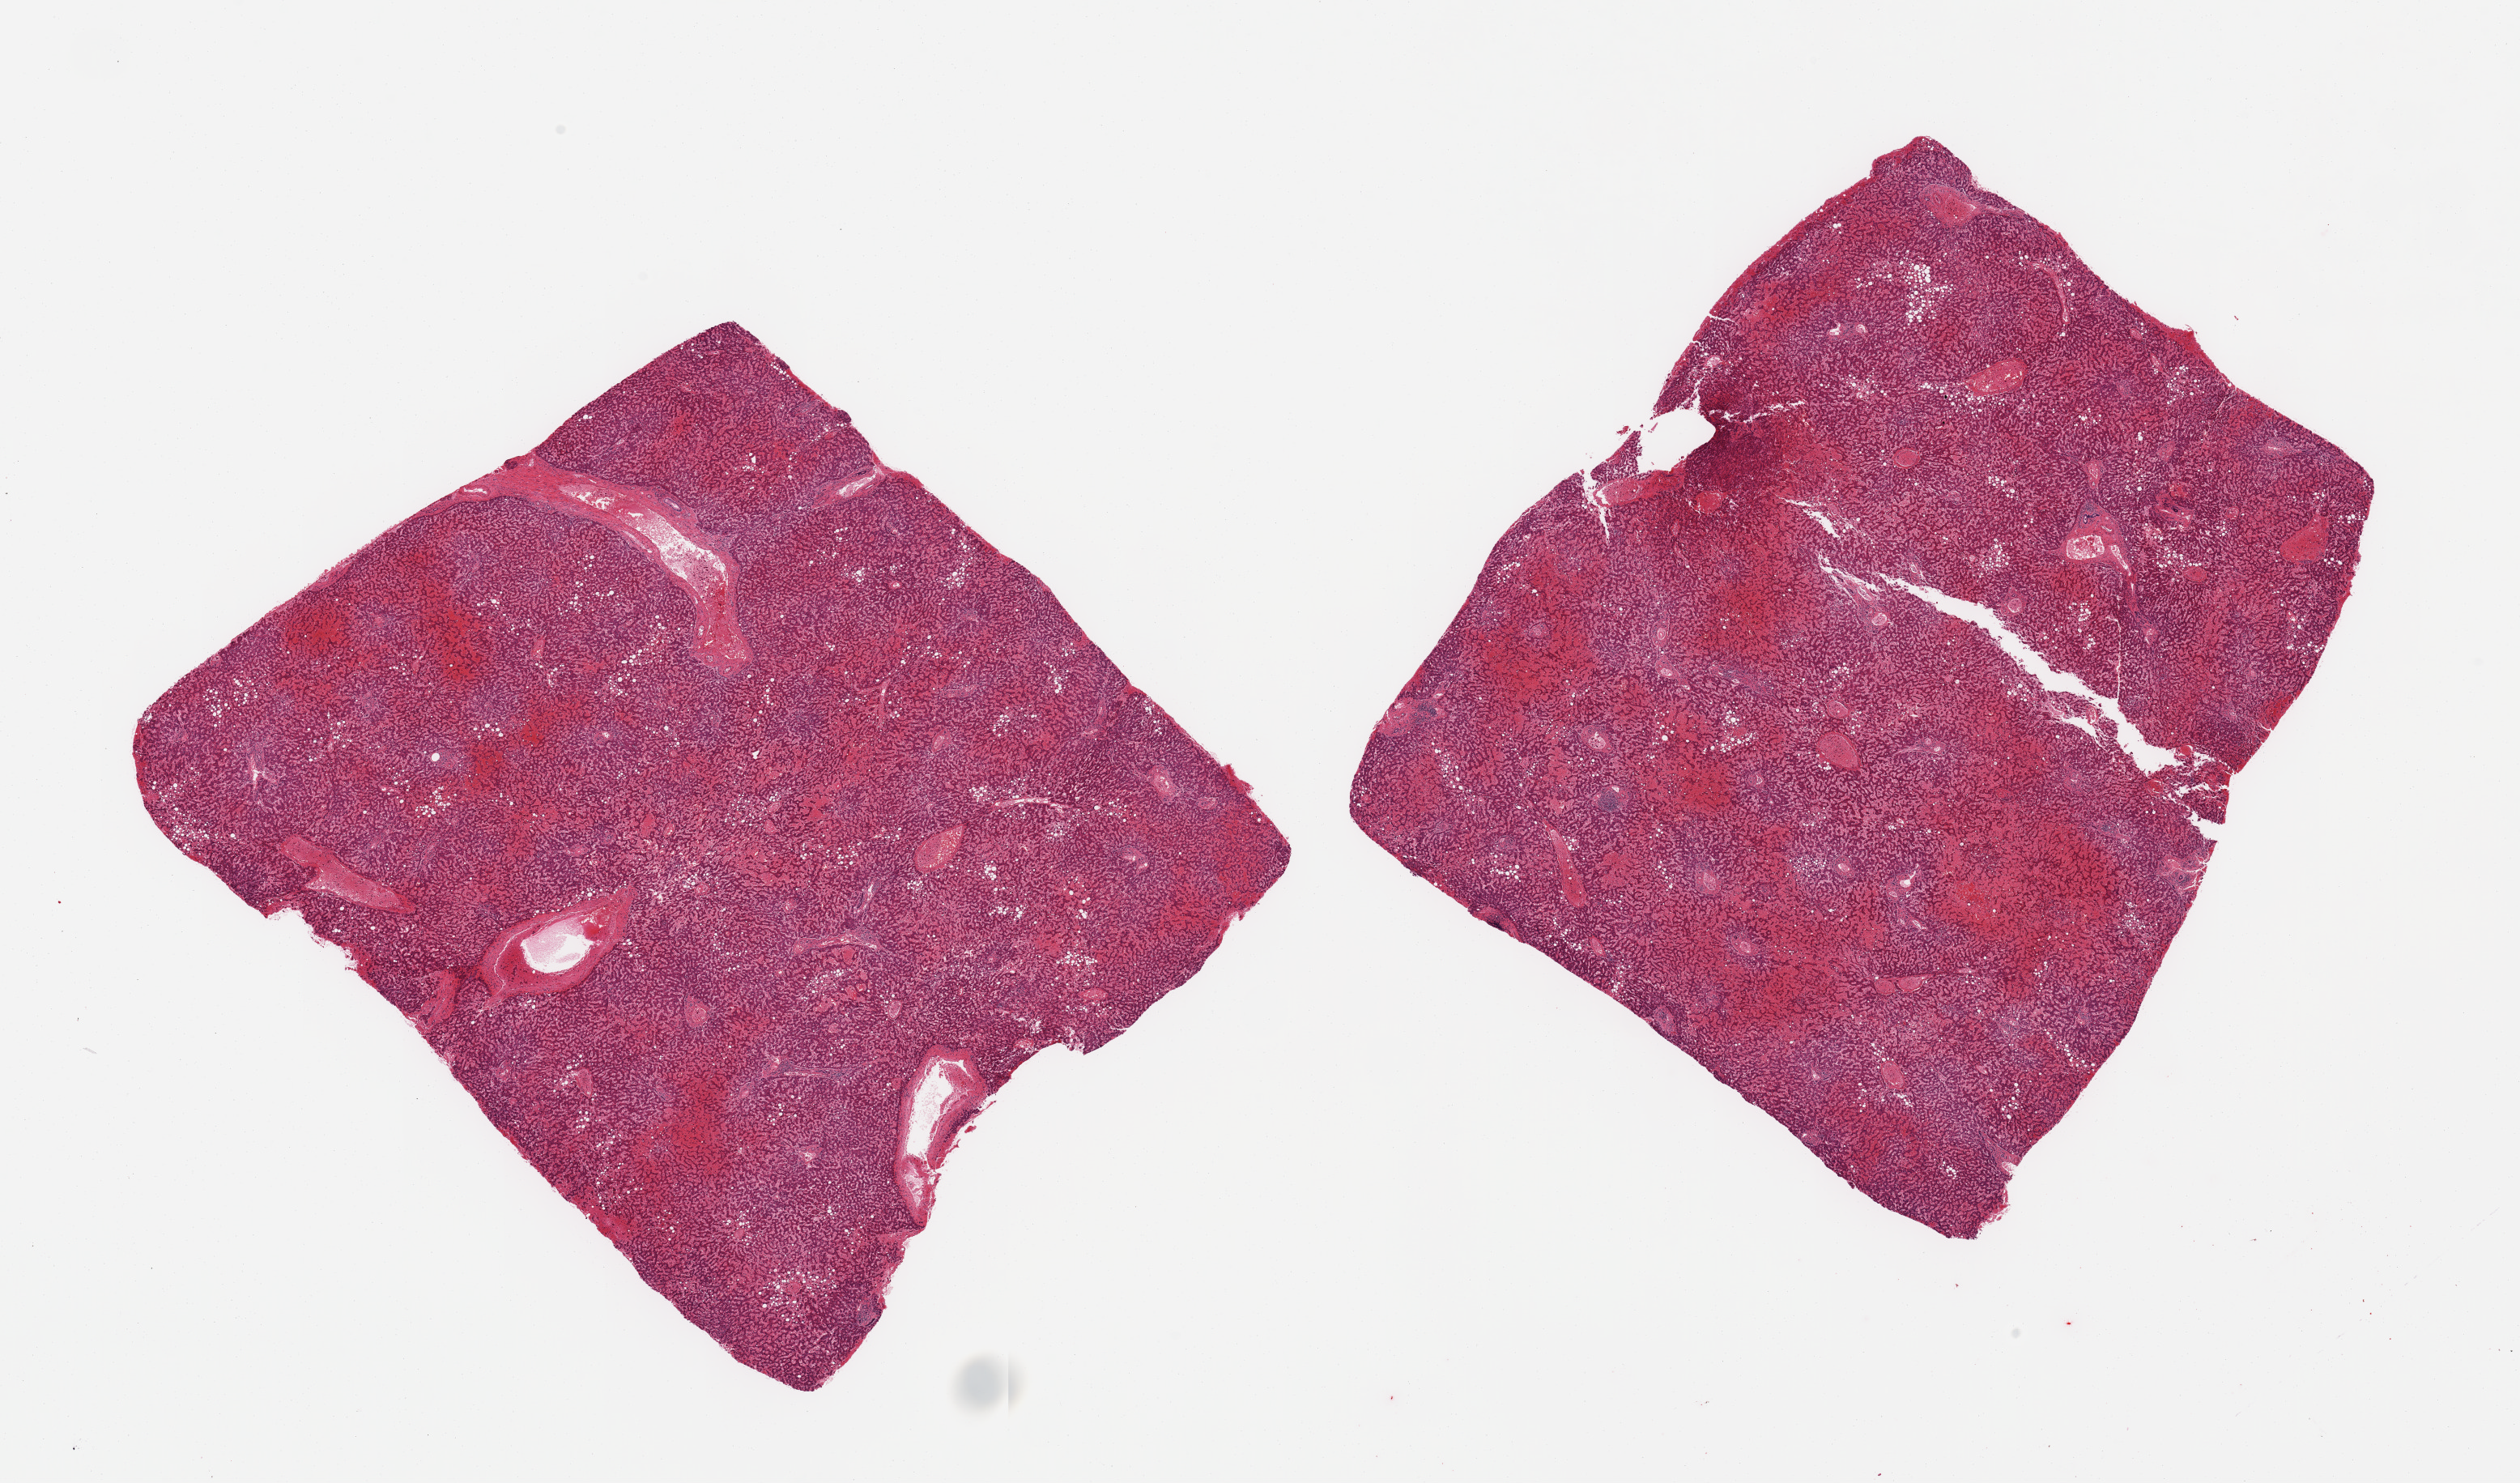
Haematoxylin and eosin whole-slide image — a low-resolution overview of the entire scanned area, about 24.6 x 14.5 mm (acquisition: 20x scan). PAXgene-fixed, paraffin-embedded tissue. Section of liver (target tissue). Tissue donor sample.
• reviewer comment on this tissue sample: 2 pieces, marked passive congestion, approaching hemorrhagic infarcts; macrovesicular steatosis involves ~20% of parenchyma